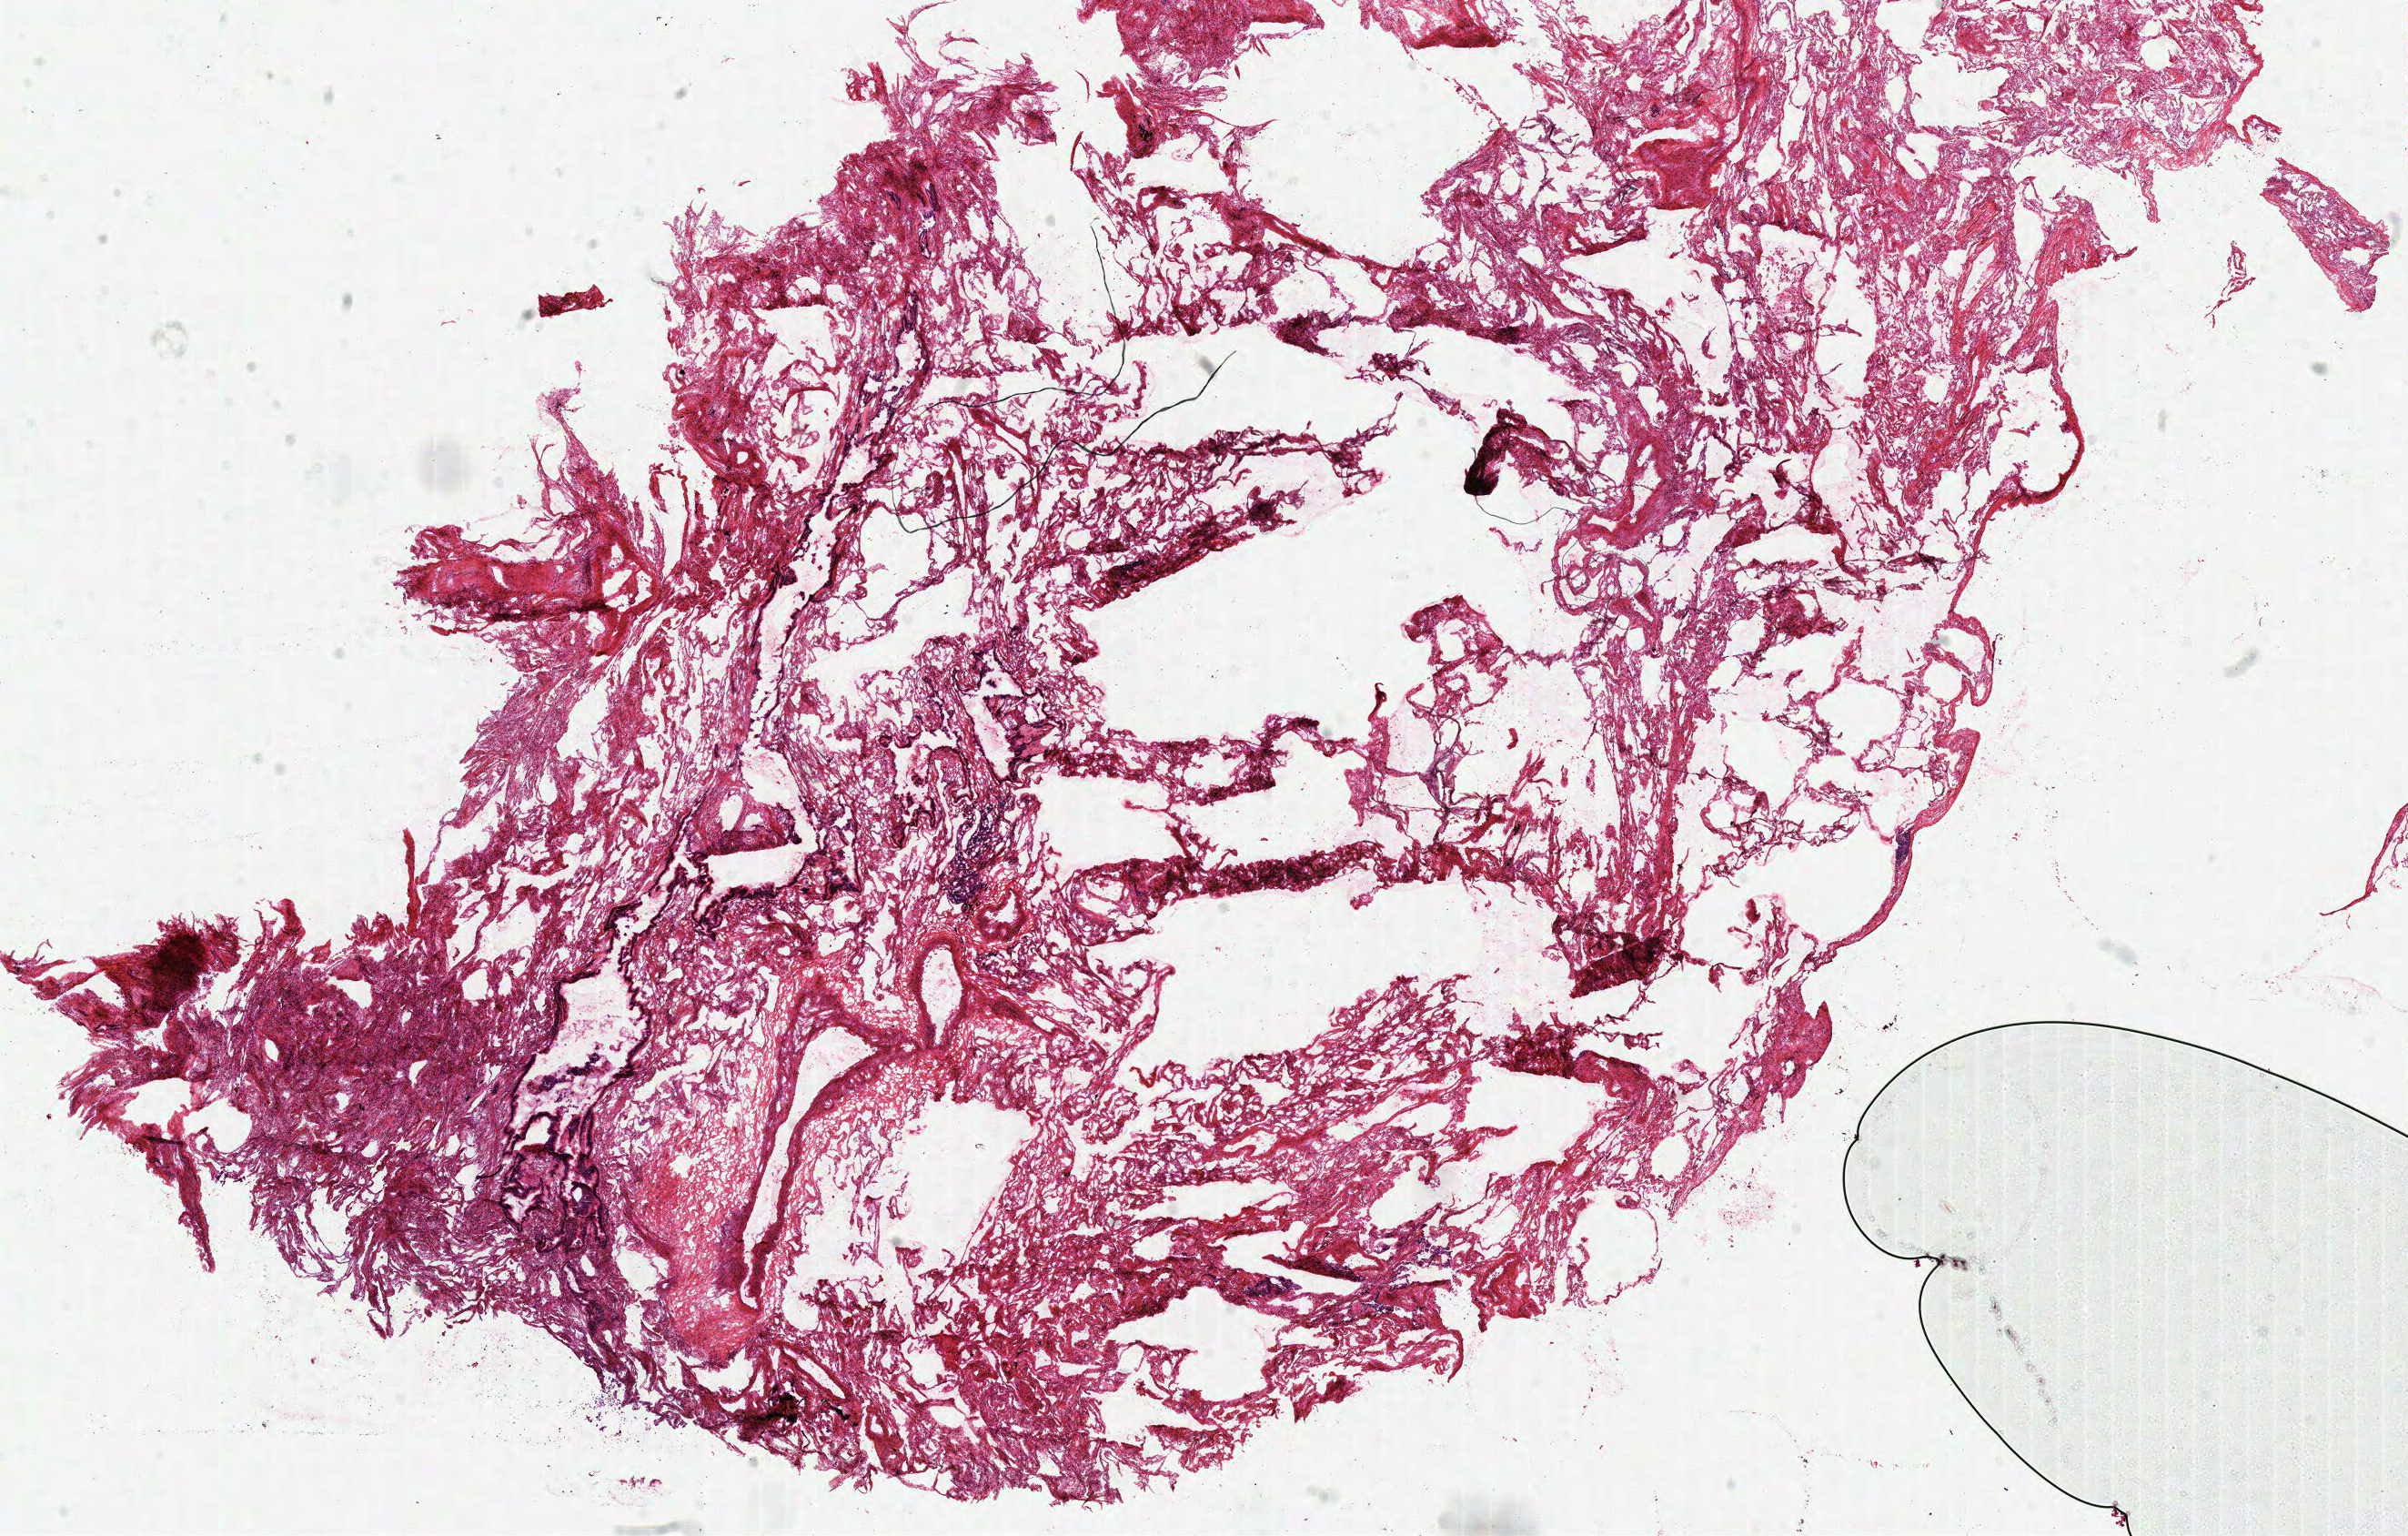
Whole-slide histology image, H&E-stained, whole scanned area (about 20.9 x 13.3 mm, from a 40x scan) shown as a low-resolution overview. Frozen section from the top of the tissue portion. Sample: solid tissue normal (non-tumour tissue), lung. Female patient; age at initial diagnosis 72 years.
This section: solid tissue normal (non-tumour) sample from the same patient. Patient diagnosis: Adenocarcinoma, NOS.